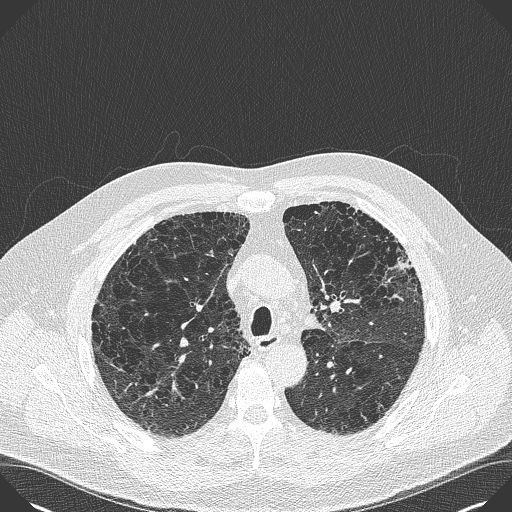
Chest CT (low-dose screening protocol), one axial image. First (baseline) screen. Lung window (W 1500 / L -600 HU). 1 mm slice thickness. 120 kVp. Slice 124 of 383 in the series. Male participant, aged 59 years at enrolment. Current smoker at enrolment.
Expert-annotated lung lesion, bounding box (x1, y1, x2, y2) in pixels: (376, 237, 427, 288). Screening reader's record for this exam: no non-calcified nodule ≥4 mm recorded. Official screen result: negative screen, minor abnormalities not suspicious for lung cancer. Lung cancer was diagnosed 909 days after this screen (after the third annual screen): bronchiolo-alveolar carcinoma, mixed mucinous and non-mucinous, left upper lobe, stage IA (AJCC 6th edition), 20 mm at pathology.